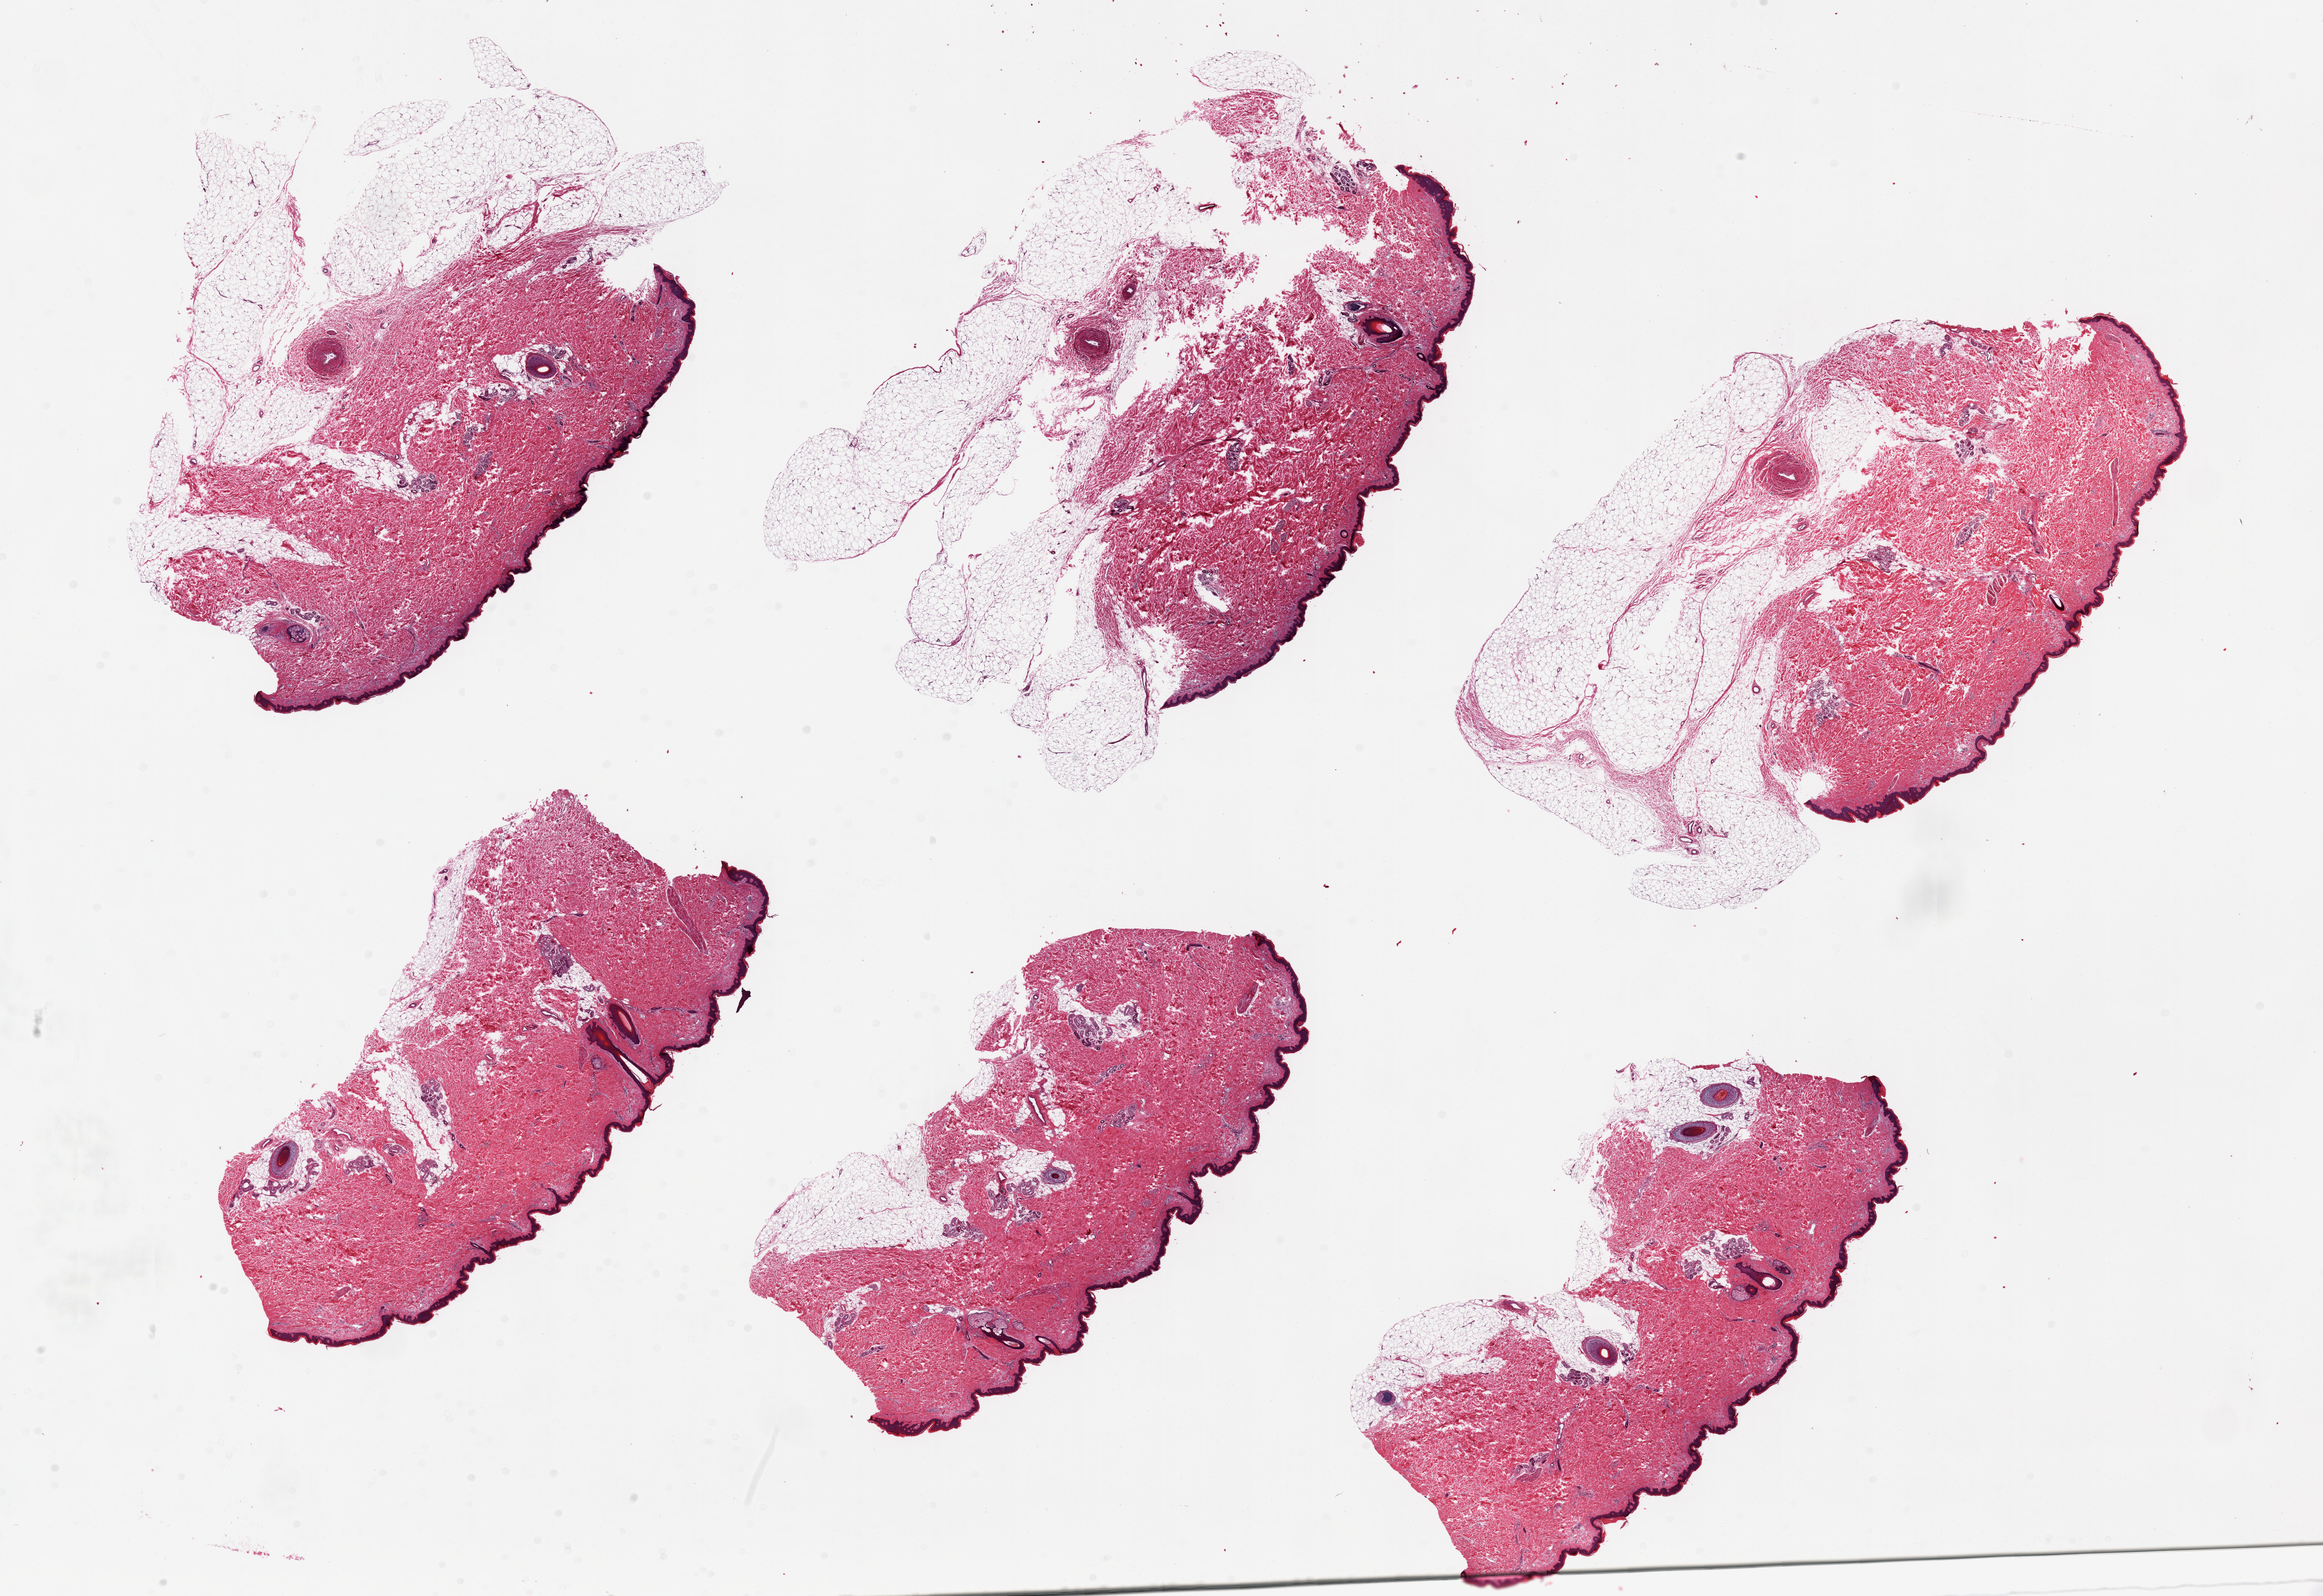
Whole-slide image, hematoxylin and eosin (H&E) stain — a low-resolution overview of the entire scanned area, about 29.5 x 20.3 mm (acquisition: 20x scan). PAXgene-fixed paraffin-embedded (PFPE) section. Target tissue: skin of lower leg. Donor tissue sample. Donor: male.
Review note (as recorded): 6 pieces; too much subcutaneous fat on 4 of 6.